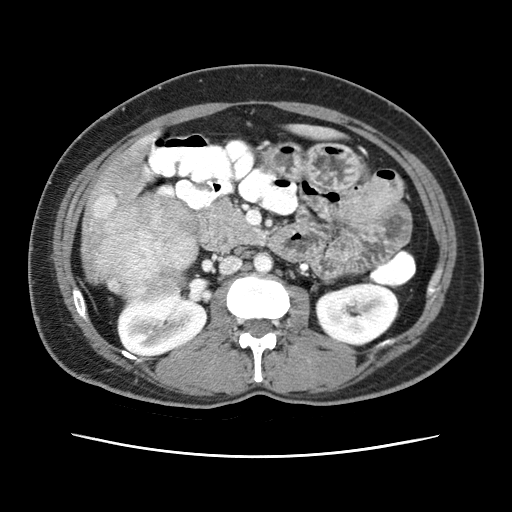
Contrast-enhanced abdominal CT (liver protocol), one axial slice. Position 11 of 79 along the scan axis. Reconstruction kernel STANDARD. Soft-tissue window (W 400 / L 40 HU). 2.5 mm slice thickness. 512 × 512 image matrix, field of view 340 × 340 mm. Case-level facts recorded for this patient, not image findings: diagnosis: hepatocellular carcinoma (patient treated with transarterial chemoembolisation; whether this scan precedes or follows treatment is not stated here); TNM stage (as recorded): Stage-I; Child-Pugh class: A; tumour differentiation: moderately differentiated.
Annotated regions visible in this slice (semi-automatic segmentation, software-assisted and operator-edited):
- abdominal aorta: bounding box <254,253,273,273> (left, top, right, bottom; pixels)
- liver parenchyma outside the tumour (the mass and vessels are separate outlines, so this box may not span the whole liver): <89,152,266,278>
- mass: <80,186,200,300>